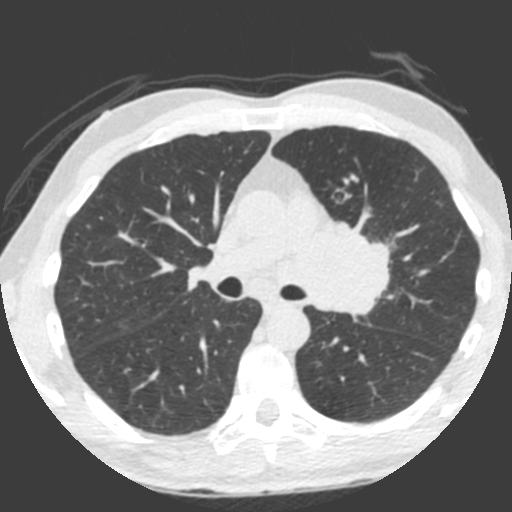
Low-dose screening chest CT, one axial slice. Slice 135 of 212 in the series (ordered by position). 120 kVp. Lung window (W 1500 / L -600 HU). 512 × 512 image matrix.
Structures marked on this image (expert manual segmentation):
- lesion 1 (tumor, upper lobe of left lung): bounding box (x1, y1, x2, y2) in pixels: (313, 221, 390, 315)